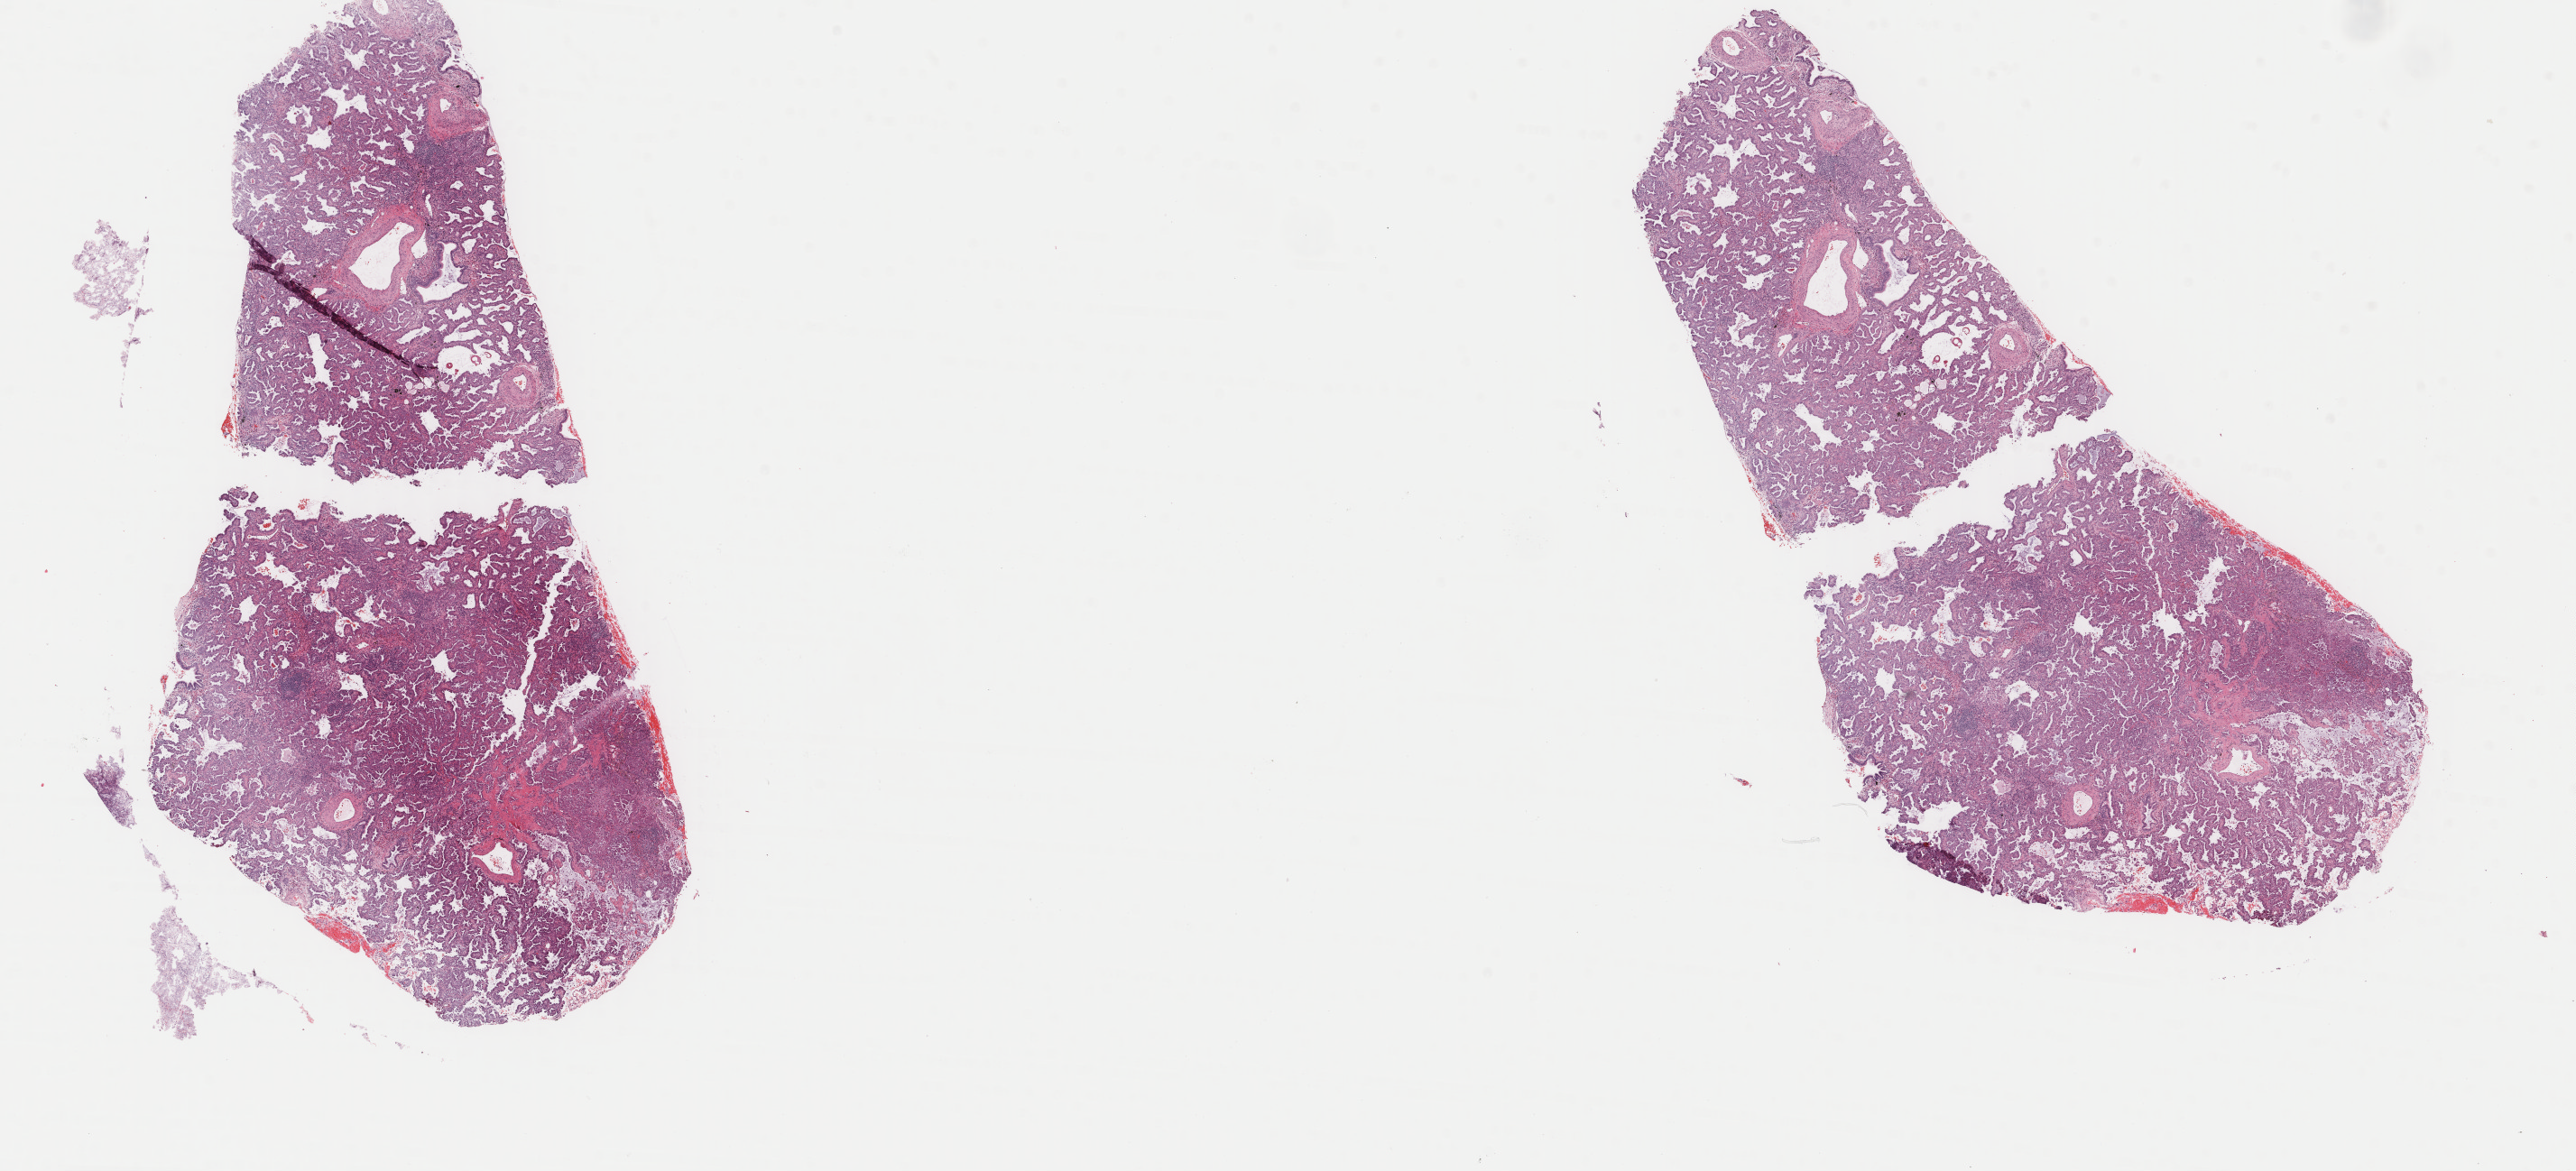
Digitized H&E tissue section (whole slide) — shown as a low-resolution overview of the whole scanned area (about 22.7 x 10.3 mm, slide scanned at 40x), frozen section, sample: primary tumour, lung. Male, age 43 years at initial diagnosis. Pathologist review of this section (percent, as recorded): tumour cells 80%, tumour nuclei 80%, normal cells 0%, stromal cells 15%, necrosis 5%. Inflammatory infiltration, as recorded: lymphocyte infiltration 0%, monocyte infiltration 0%, neutrophil infiltration 0%.
Pathologic diagnosis: Adenocarcinoma, NOS (upper lobe, lung). AJCC pathologic stage: IB (6th edition). TNM: T2 N0 M0.